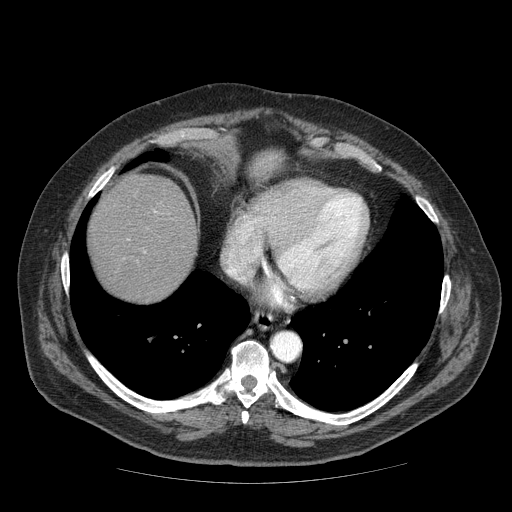
Contrast-enhanced abdominal CT (liver protocol), one axial slice. Slice 66 of 85 in the series (ordered by position). Reconstruction kernel STANDARD. 120 kVp. Soft-tissue window (W 400 / L 40 HU). 2.5 mm slice thickness. 512 × 512 image matrix, field of view 420 × 420 mm. From the clinical record (not read from this slice): diagnosis: hepatocellular carcinoma (patient treated with transarterial chemoembolisation; whether this scan precedes or follows treatment is not stated here); TNM stage (as recorded): Stage-IIIA; Child-Pugh class: A; tumour nodularity: multinodular.
Structures marked on this image (semi-automatically segmented with operator editing):
- liver parenchyma outside the tumour (the mass and vessels are separate outlines, so this box may not span the whole liver): box from (x=88, y=154) to (x=278, y=302) px